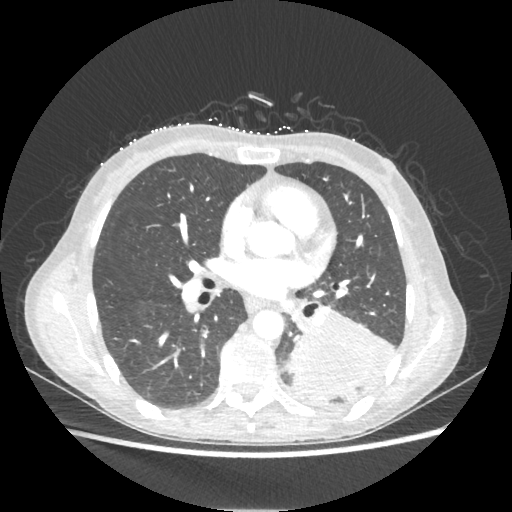
Chest CT, one axial slice. 80 kVp. Lung window (W 1500 / L -600 HU). 1.25 mm slice thickness. 512 × 512 image matrix, field of view 360 × 360 mm. Female patient, age 53 years. From the clinical record (not read from this slice): clinical TNM (as recorded): T3 N0 M0.
Structures marked on this image (bounding box drawn by a radiologist):
- lung tumour (recorded histology: adenocarcinoma): bounding box (x1, y1, x2, y2) in pixels: (288, 307, 396, 400)